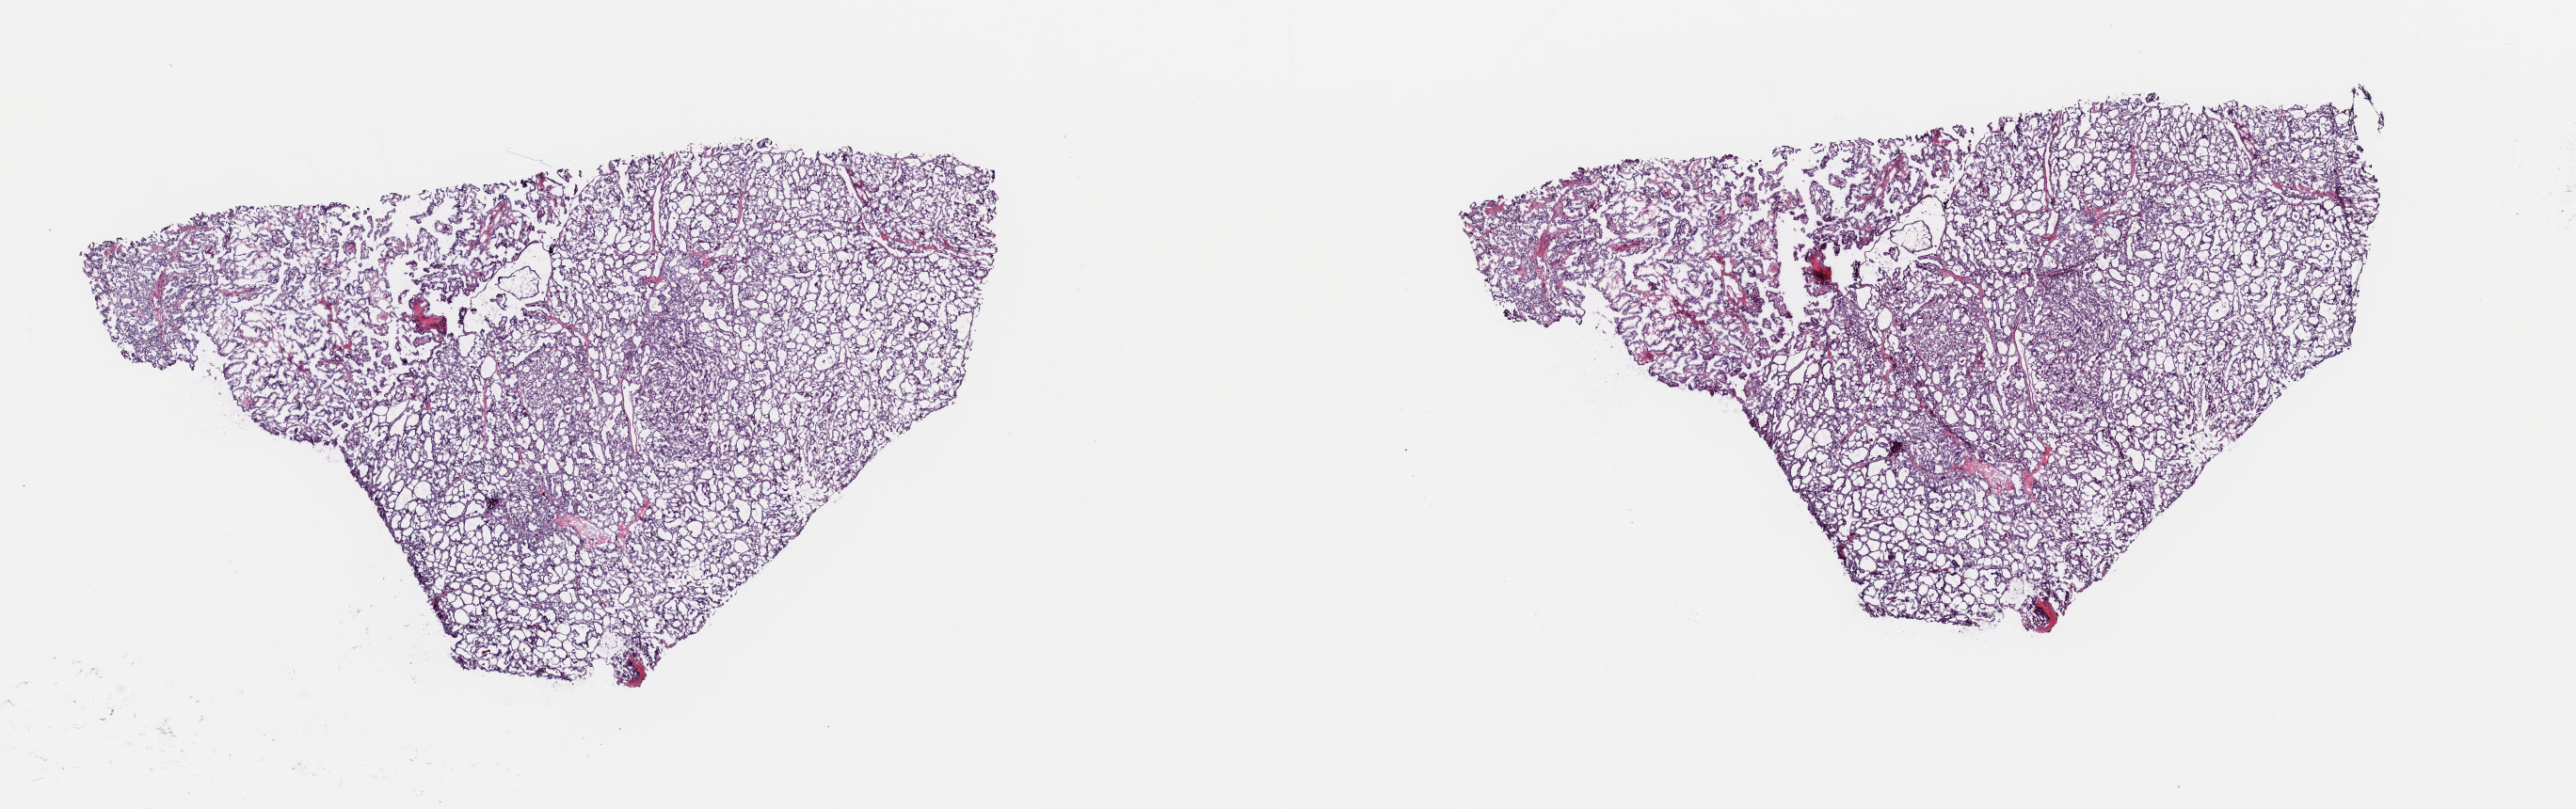
Digitized H&E-stained tissue section (whole slide) — shown as a low-resolution overview of the whole scanned area (about 21.6 x 6.8 mm, slide scanned at 40x); frozen section; thyroid, primary tumour sample. Female patient; age at initial diagnosis 34 years. Pathologist review of this section (percent, as recorded): tumour cells 100%, tumour nuclei 95%, normal cells 0%, stromal cells 0%, necrosis 0%. Infiltration values recorded for this section: lymphocyte infiltration 1%, monocyte infiltration 0%, neutrophil infiltration 0%.
AJCC pathologic stage: I. Laterality: left. Lymph nodes positive (case pathology): 0 of 3 examined. Pathologic diagnosis: Papillary adenocarcinoma, NOS (thyroid gland).